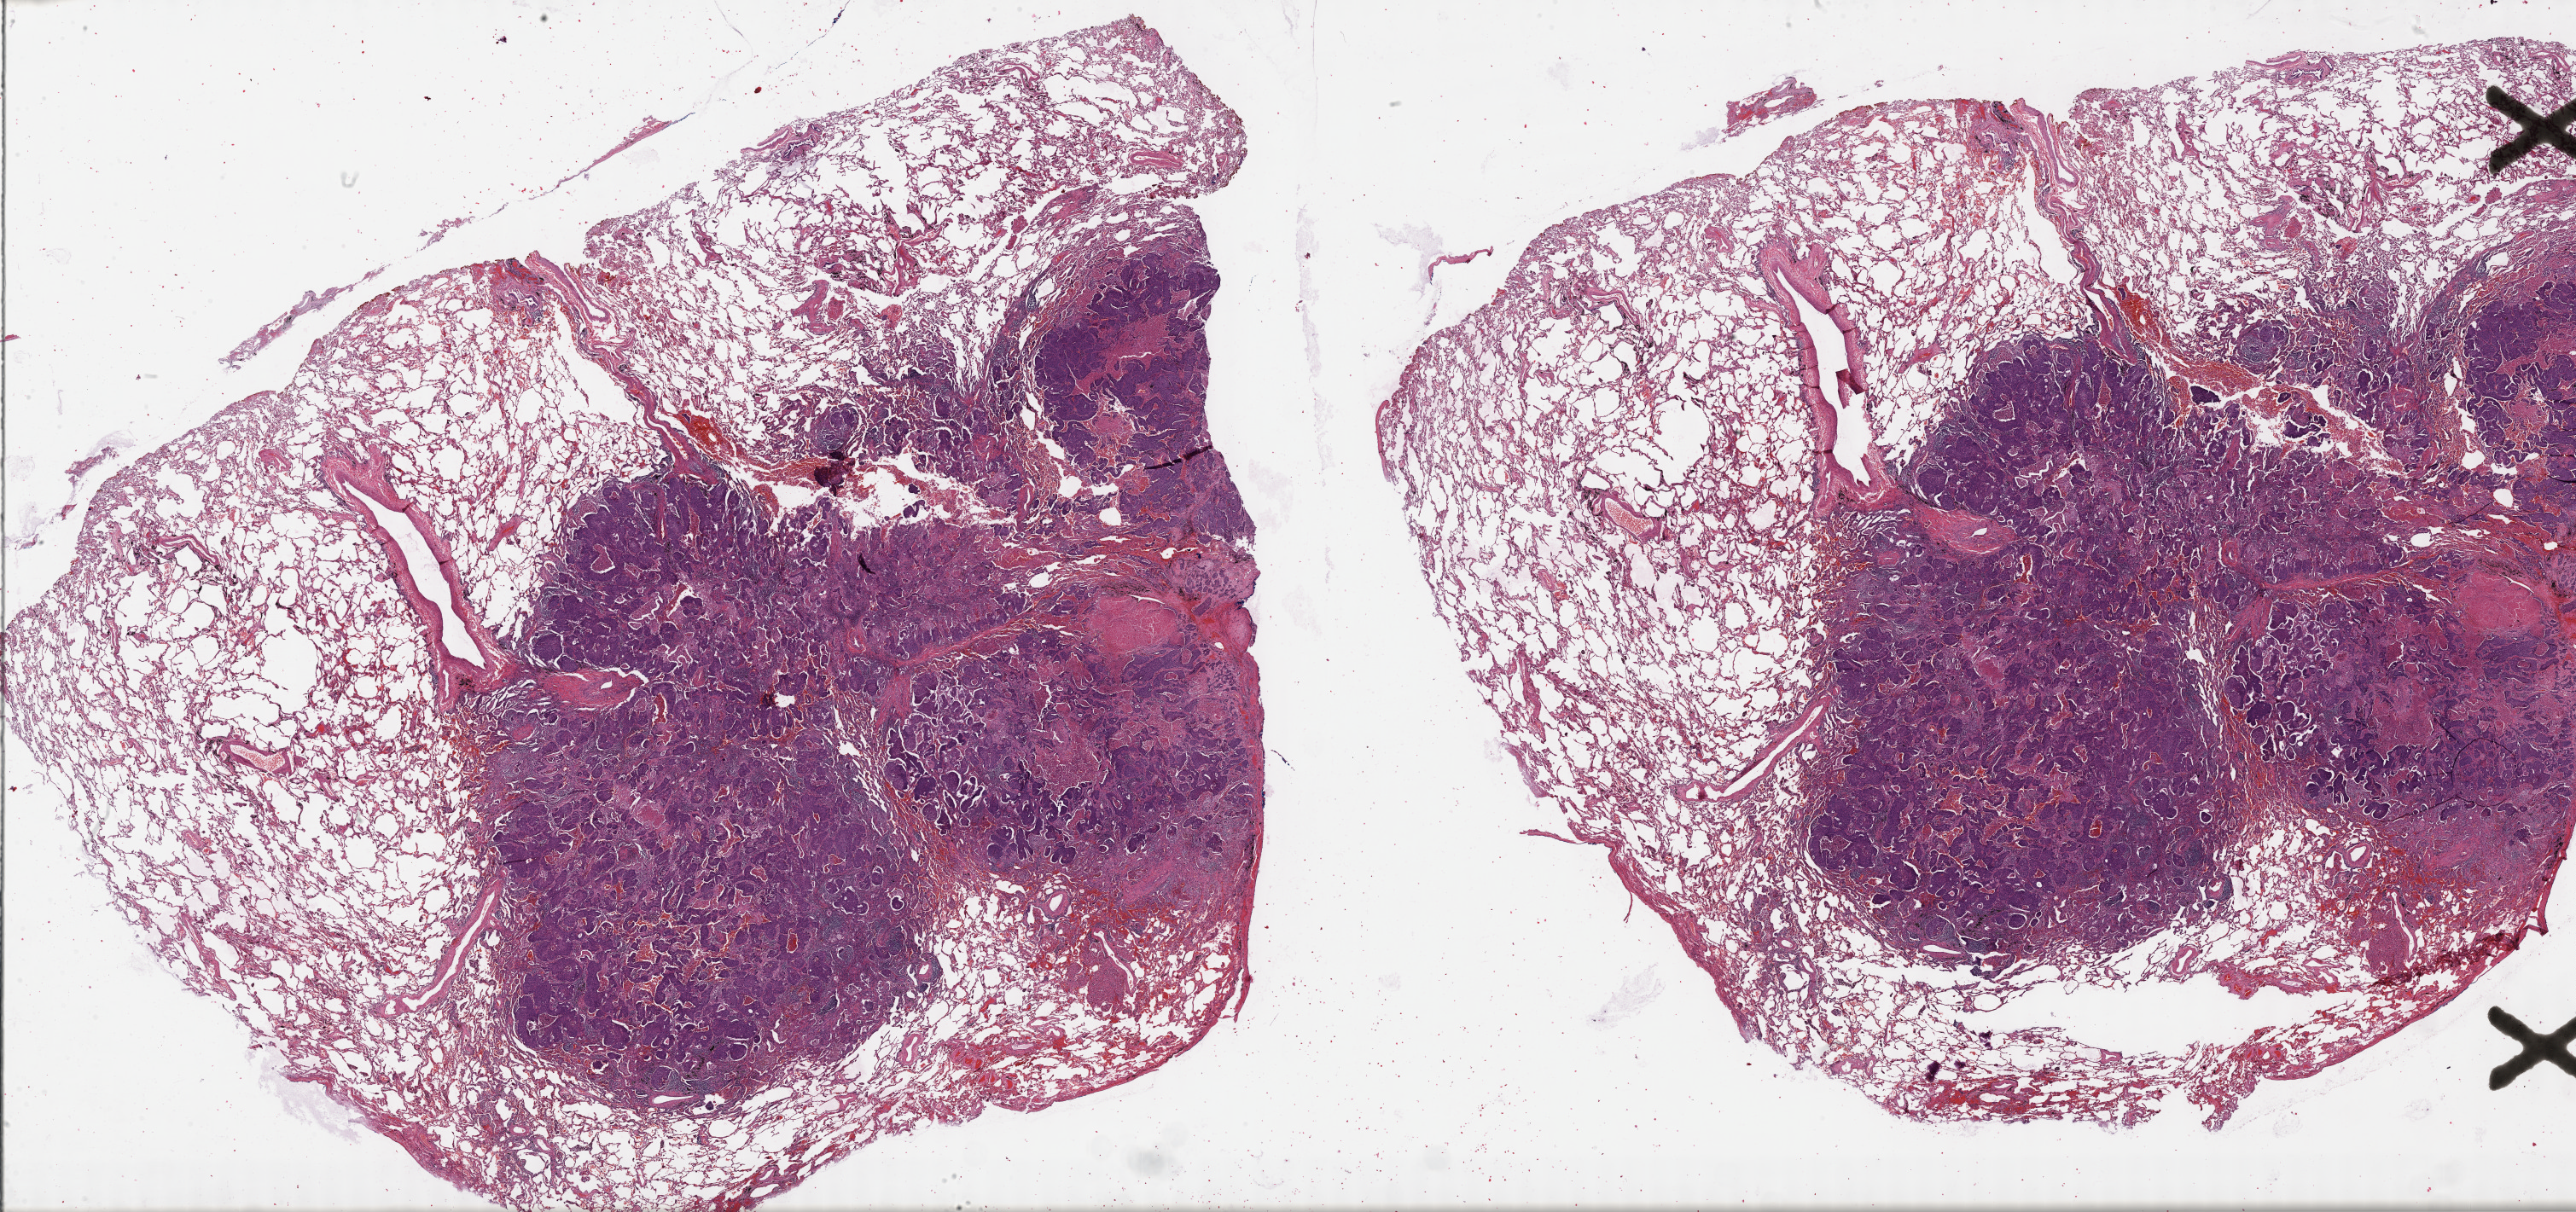
Whole-slide histology image, Hematoxylin and eosin (H&E) stained — shown as a low-resolution overview of the whole scanned area (about 48.8 x 23.0 mm), formalin-fixed paraffin-embedded (FFPE) diagnostic section, lung, primary tumour sample. Patient: male, age at initial diagnosis 77 years.
TNM: T2 N0 MX. AJCC pathologic stage: IB (6th edition). Pathologic diagnosis: Squamous cell carcinoma, NOS (upper lobe, lung). Laterality: right.